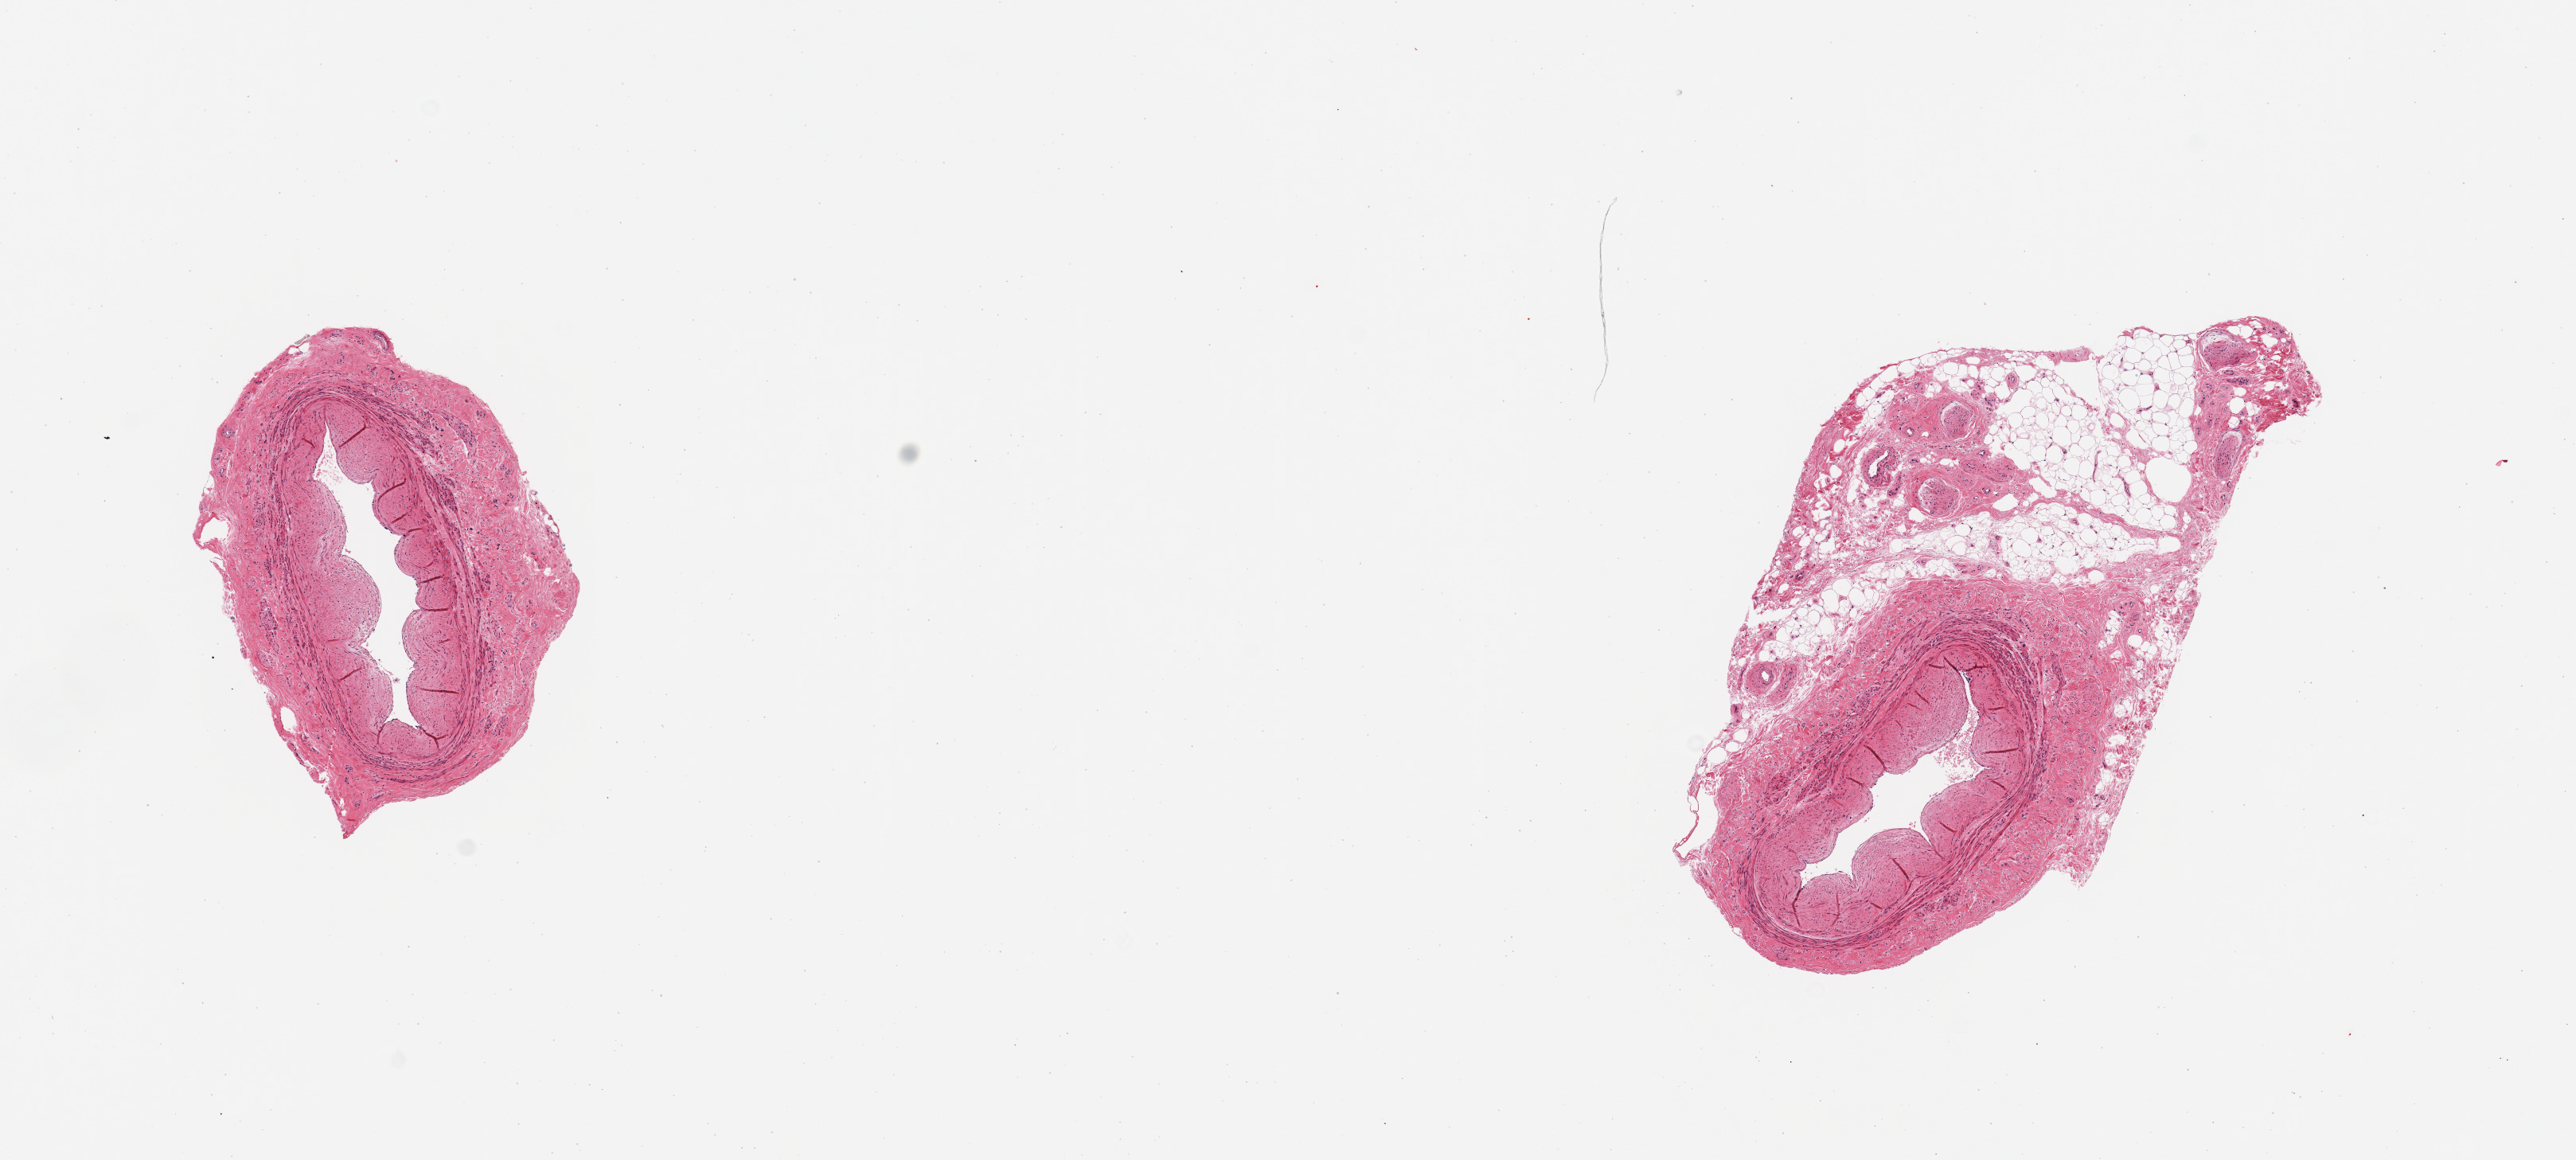
Haematoxylin and eosin whole-slide image, a low-resolution overview of the entire scanned area, about 12.8 x 5.8 mm (slide scanned at 20x); PAXgene-fixed, paraffin-embedded tissue; sampled site (target tissue): tibial artery; donor tissue sample. Donor sex: male.
• pathologist's review note for this sample: 2 pieces; one piece with adherent ~1mm fat/nerve